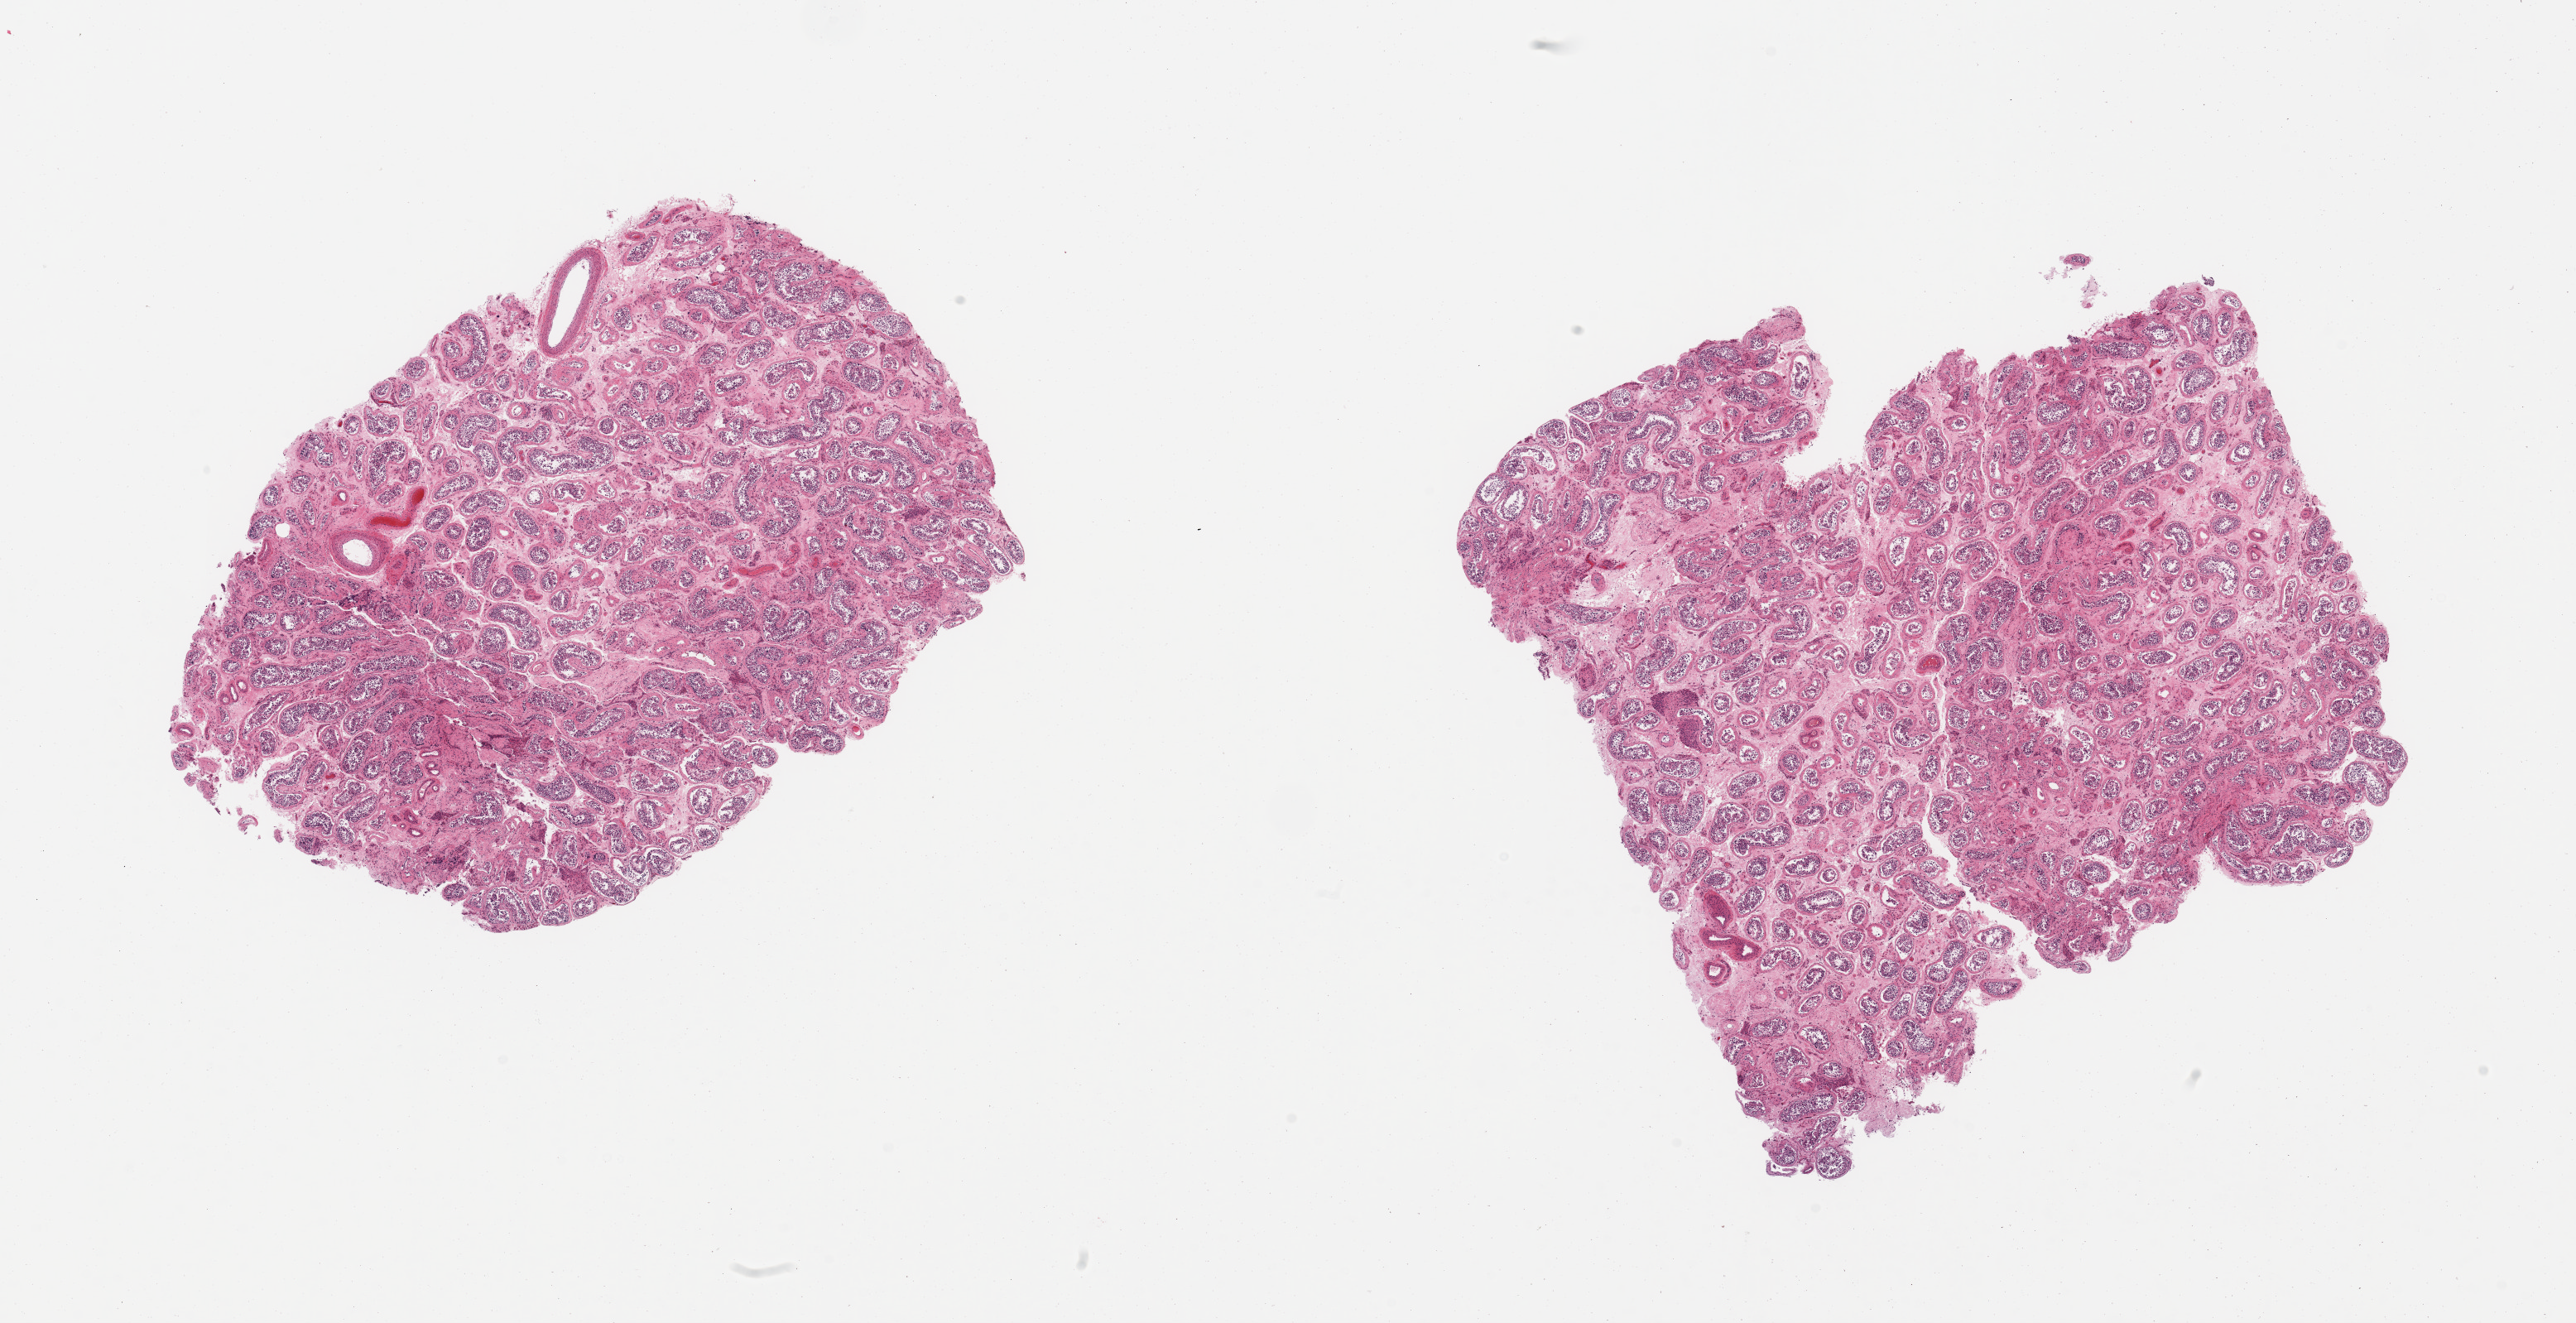
H&E whole-slide image, brightfield — shown as a low-resolution overview of the whole scanned area (about 24.6 x 12.6 mm), PAXgene-fixed paraffin-embedded (PFPE) section, sampled site (target tissue): testis, donor tissue sample.
- pathologist's review note for this sample: 2 pieces; interstitial fibrosis with scarring; significantly decreased spermatogenesis; thick walled vessels; congestion